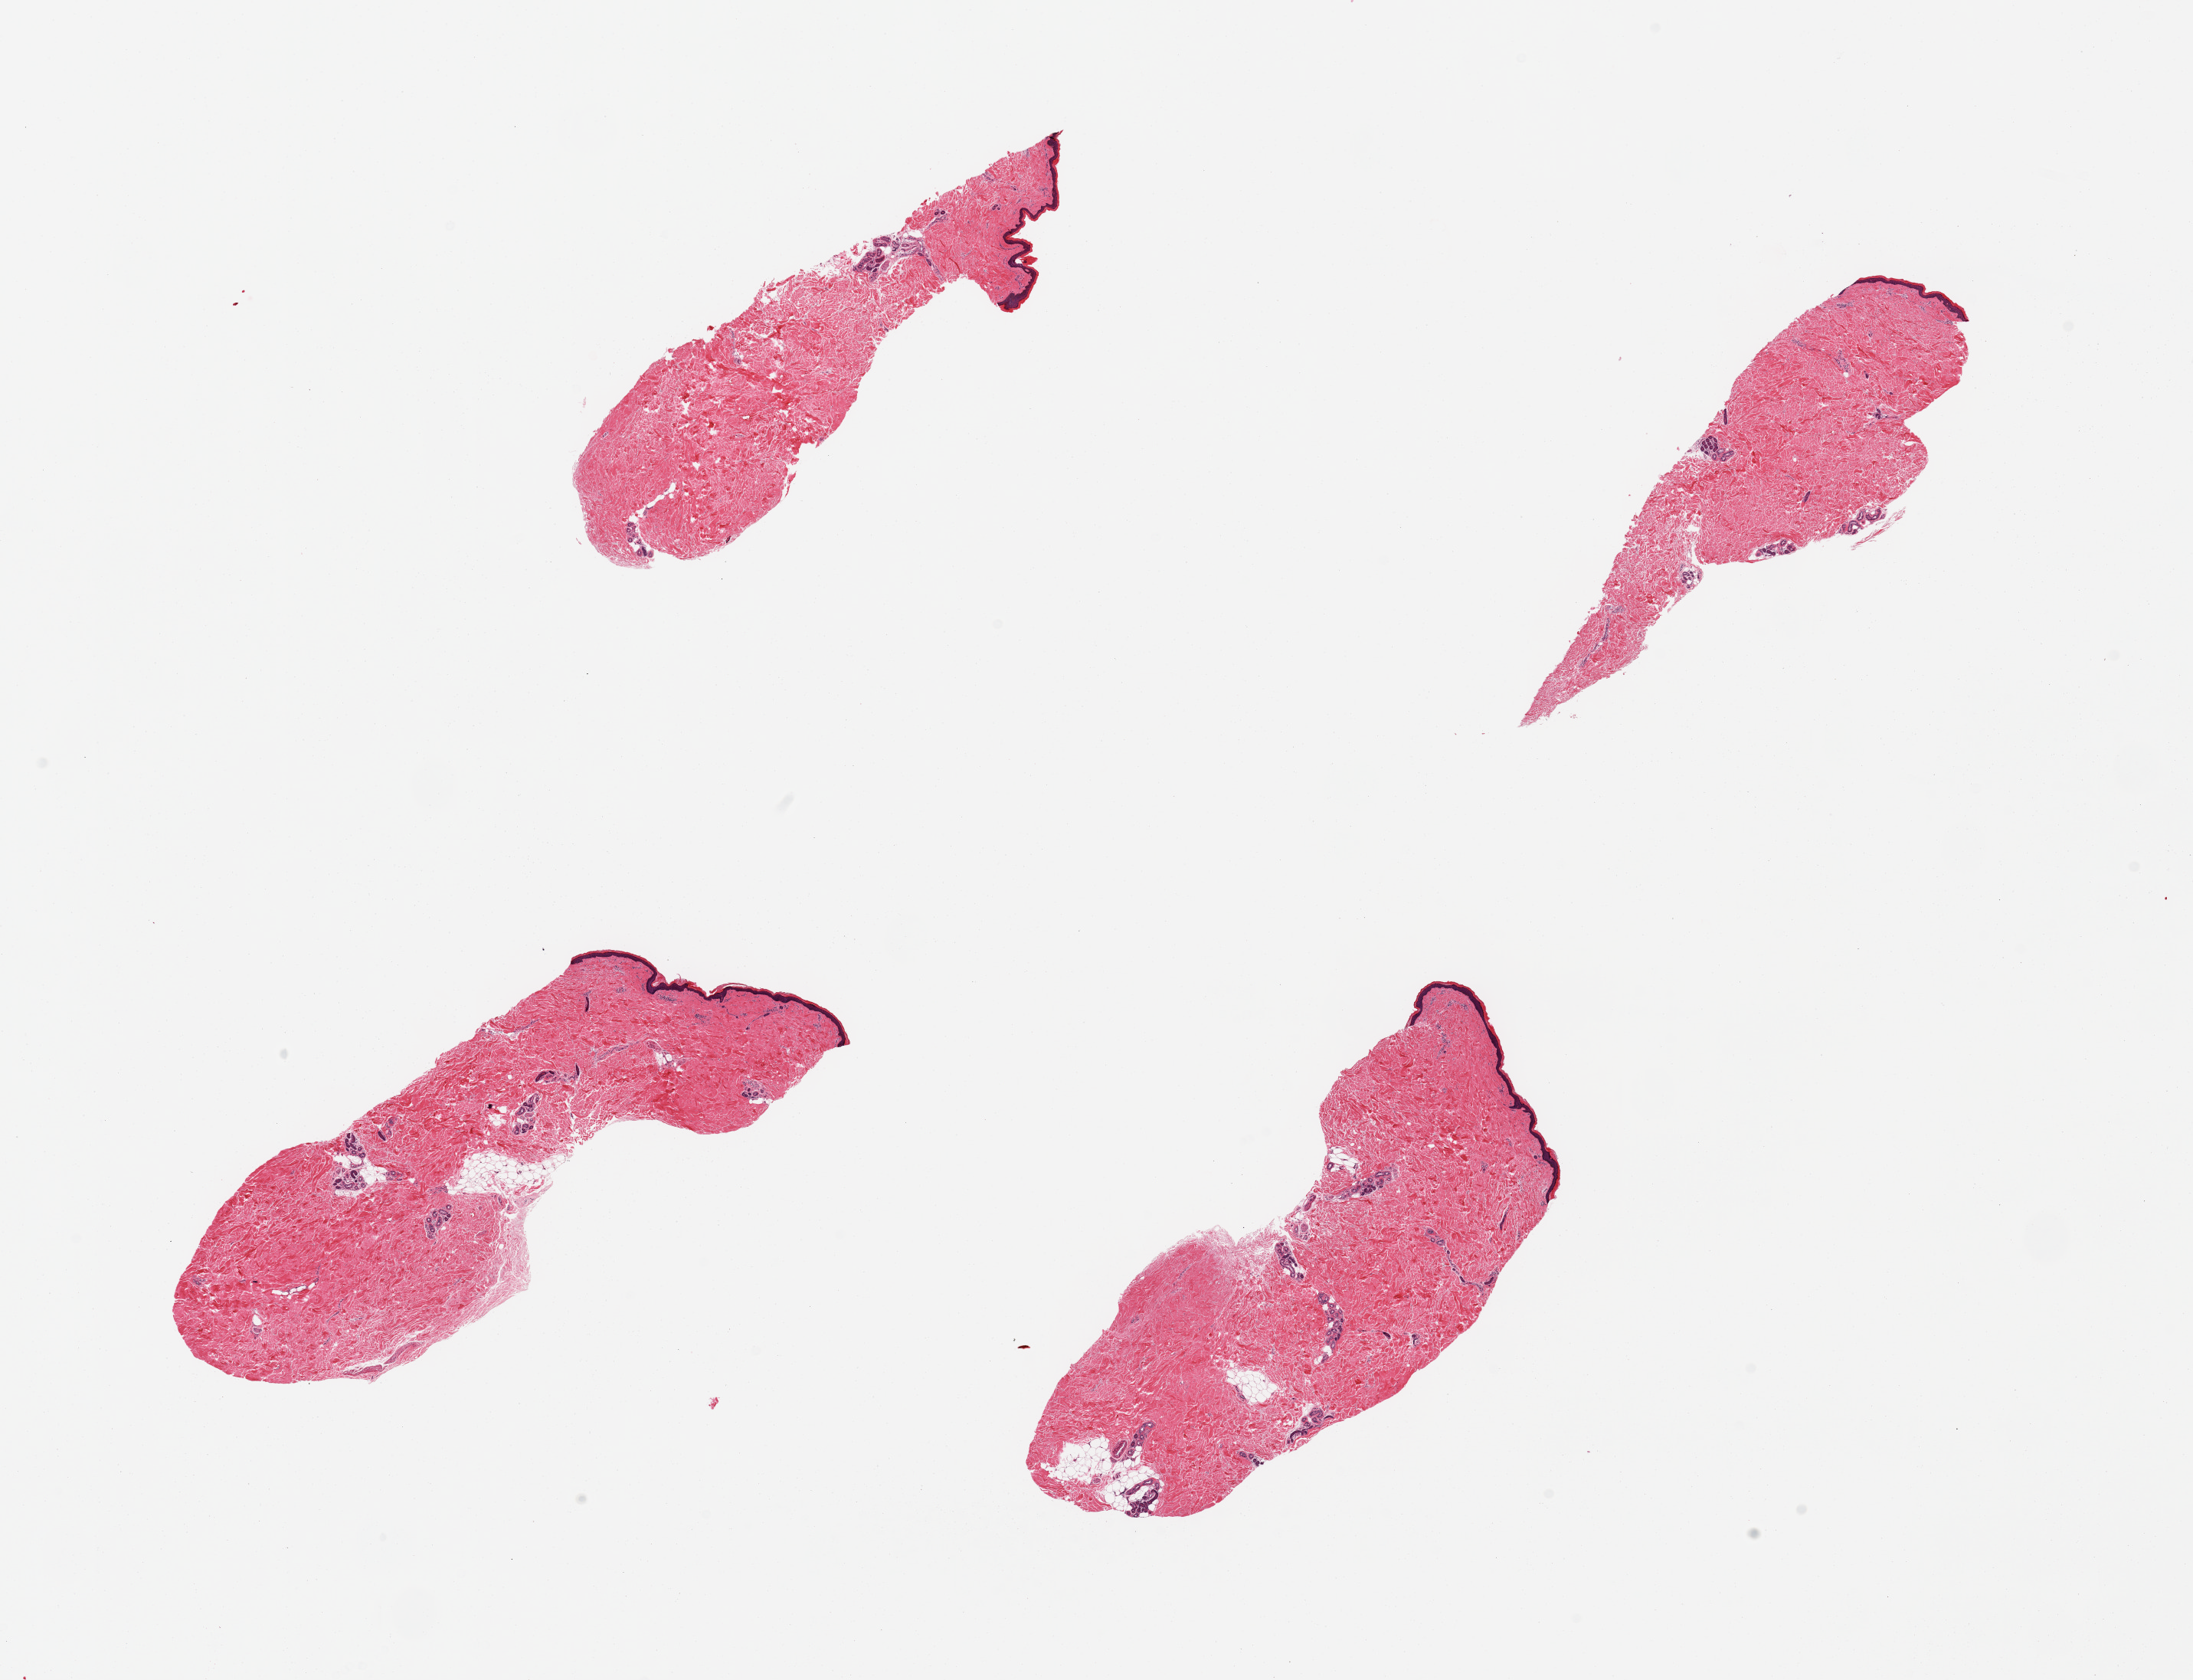
Hematoxylin and eosin (H&E) whole-slide image, brightfield, shown as a low-resolution overview of the whole scanned area (about 22.6 x 17.3 mm), PAXgene-fixed, paraffin-embedded tissue, section of skin of lower leg (target tissue), donor tissue sample. Donor sex: male.
Pathologist's review note for this sample: 4 pieces; up to 10% intradermal fat.